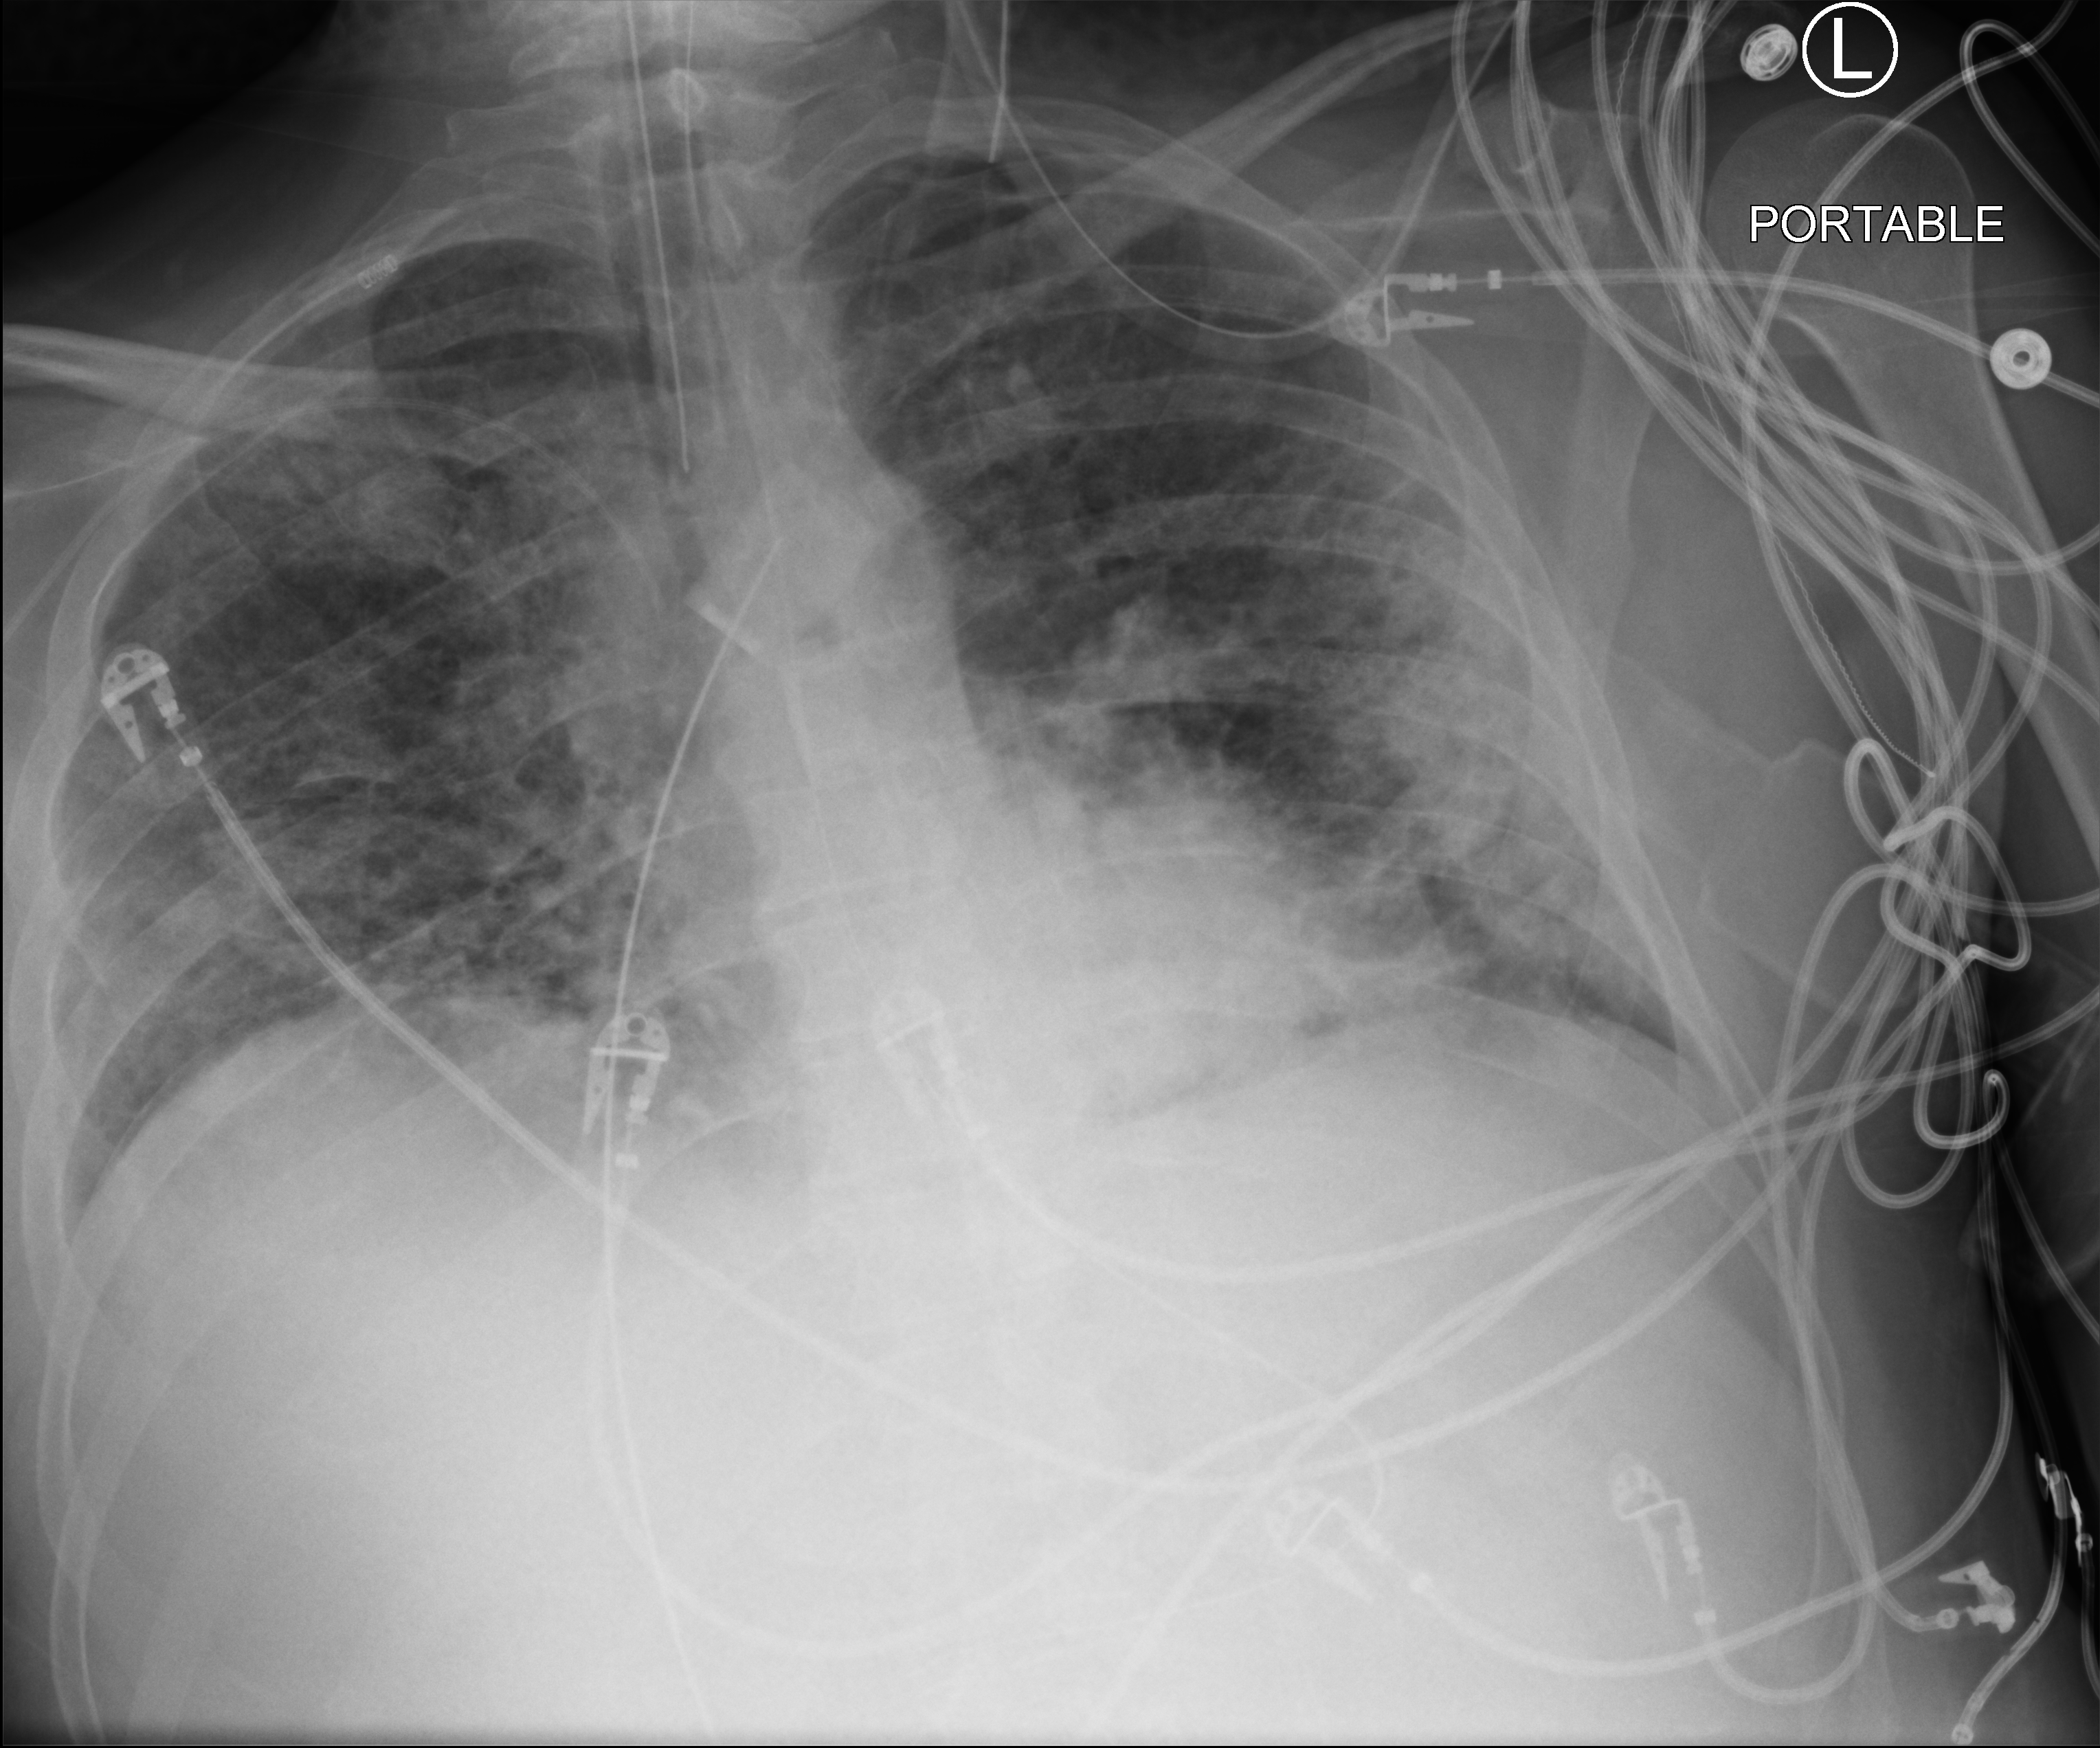
Portable chest radiograph, anteroposterior (AP) projection. Patient hospitalised with COVID-19; male, aged 18–59 years.
Admission-level facts for this patient (not findings on this image; timing relative to this image not recorded): mechanically ventilated during this hospital stay: yes; diabetes (admission record): no; COPD (admission record): no.